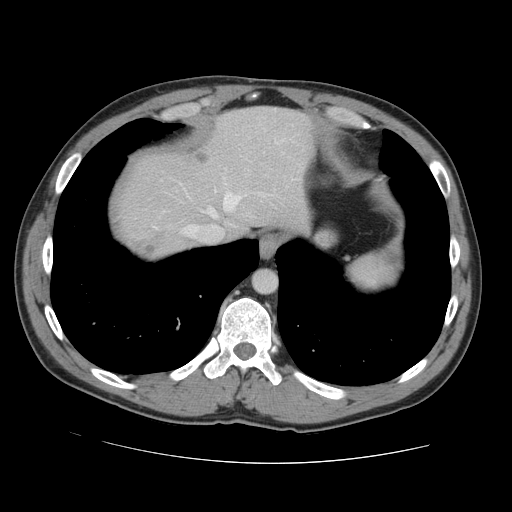
Contrast-enhanced abdominal CT, one axial slice. Position 121 of 131 along the scan axis. Intravenous contrast given. Soft-tissue window (W 400 / L 40 HU). 2.5 mm slice thickness. 512 × 512 image matrix, field of view 380 × 380 mm. Male patient, age 40 years. From the clinical record (not read from this slice): diagnosis: colorectal cancer liver metastases, imaged before liver resection; multiple liver metastases: yes; largest metastasis: 2.9 cm; disease in both lobes: yes.
Structures marked on this image (manually delineated by an expert):
- hepatic veins: box from (x=185, y=193) to (x=265, y=236) px
- liver: (x=121, y=107)–(x=311, y=257)
- planned liver remnant (the part of the liver to remain after resection): (x=132, y=107)–(x=311, y=236)
- liver metastasis: (x=195, y=152)–(x=209, y=162)
- liver metastasis: (x=147, y=248)–(x=157, y=255)